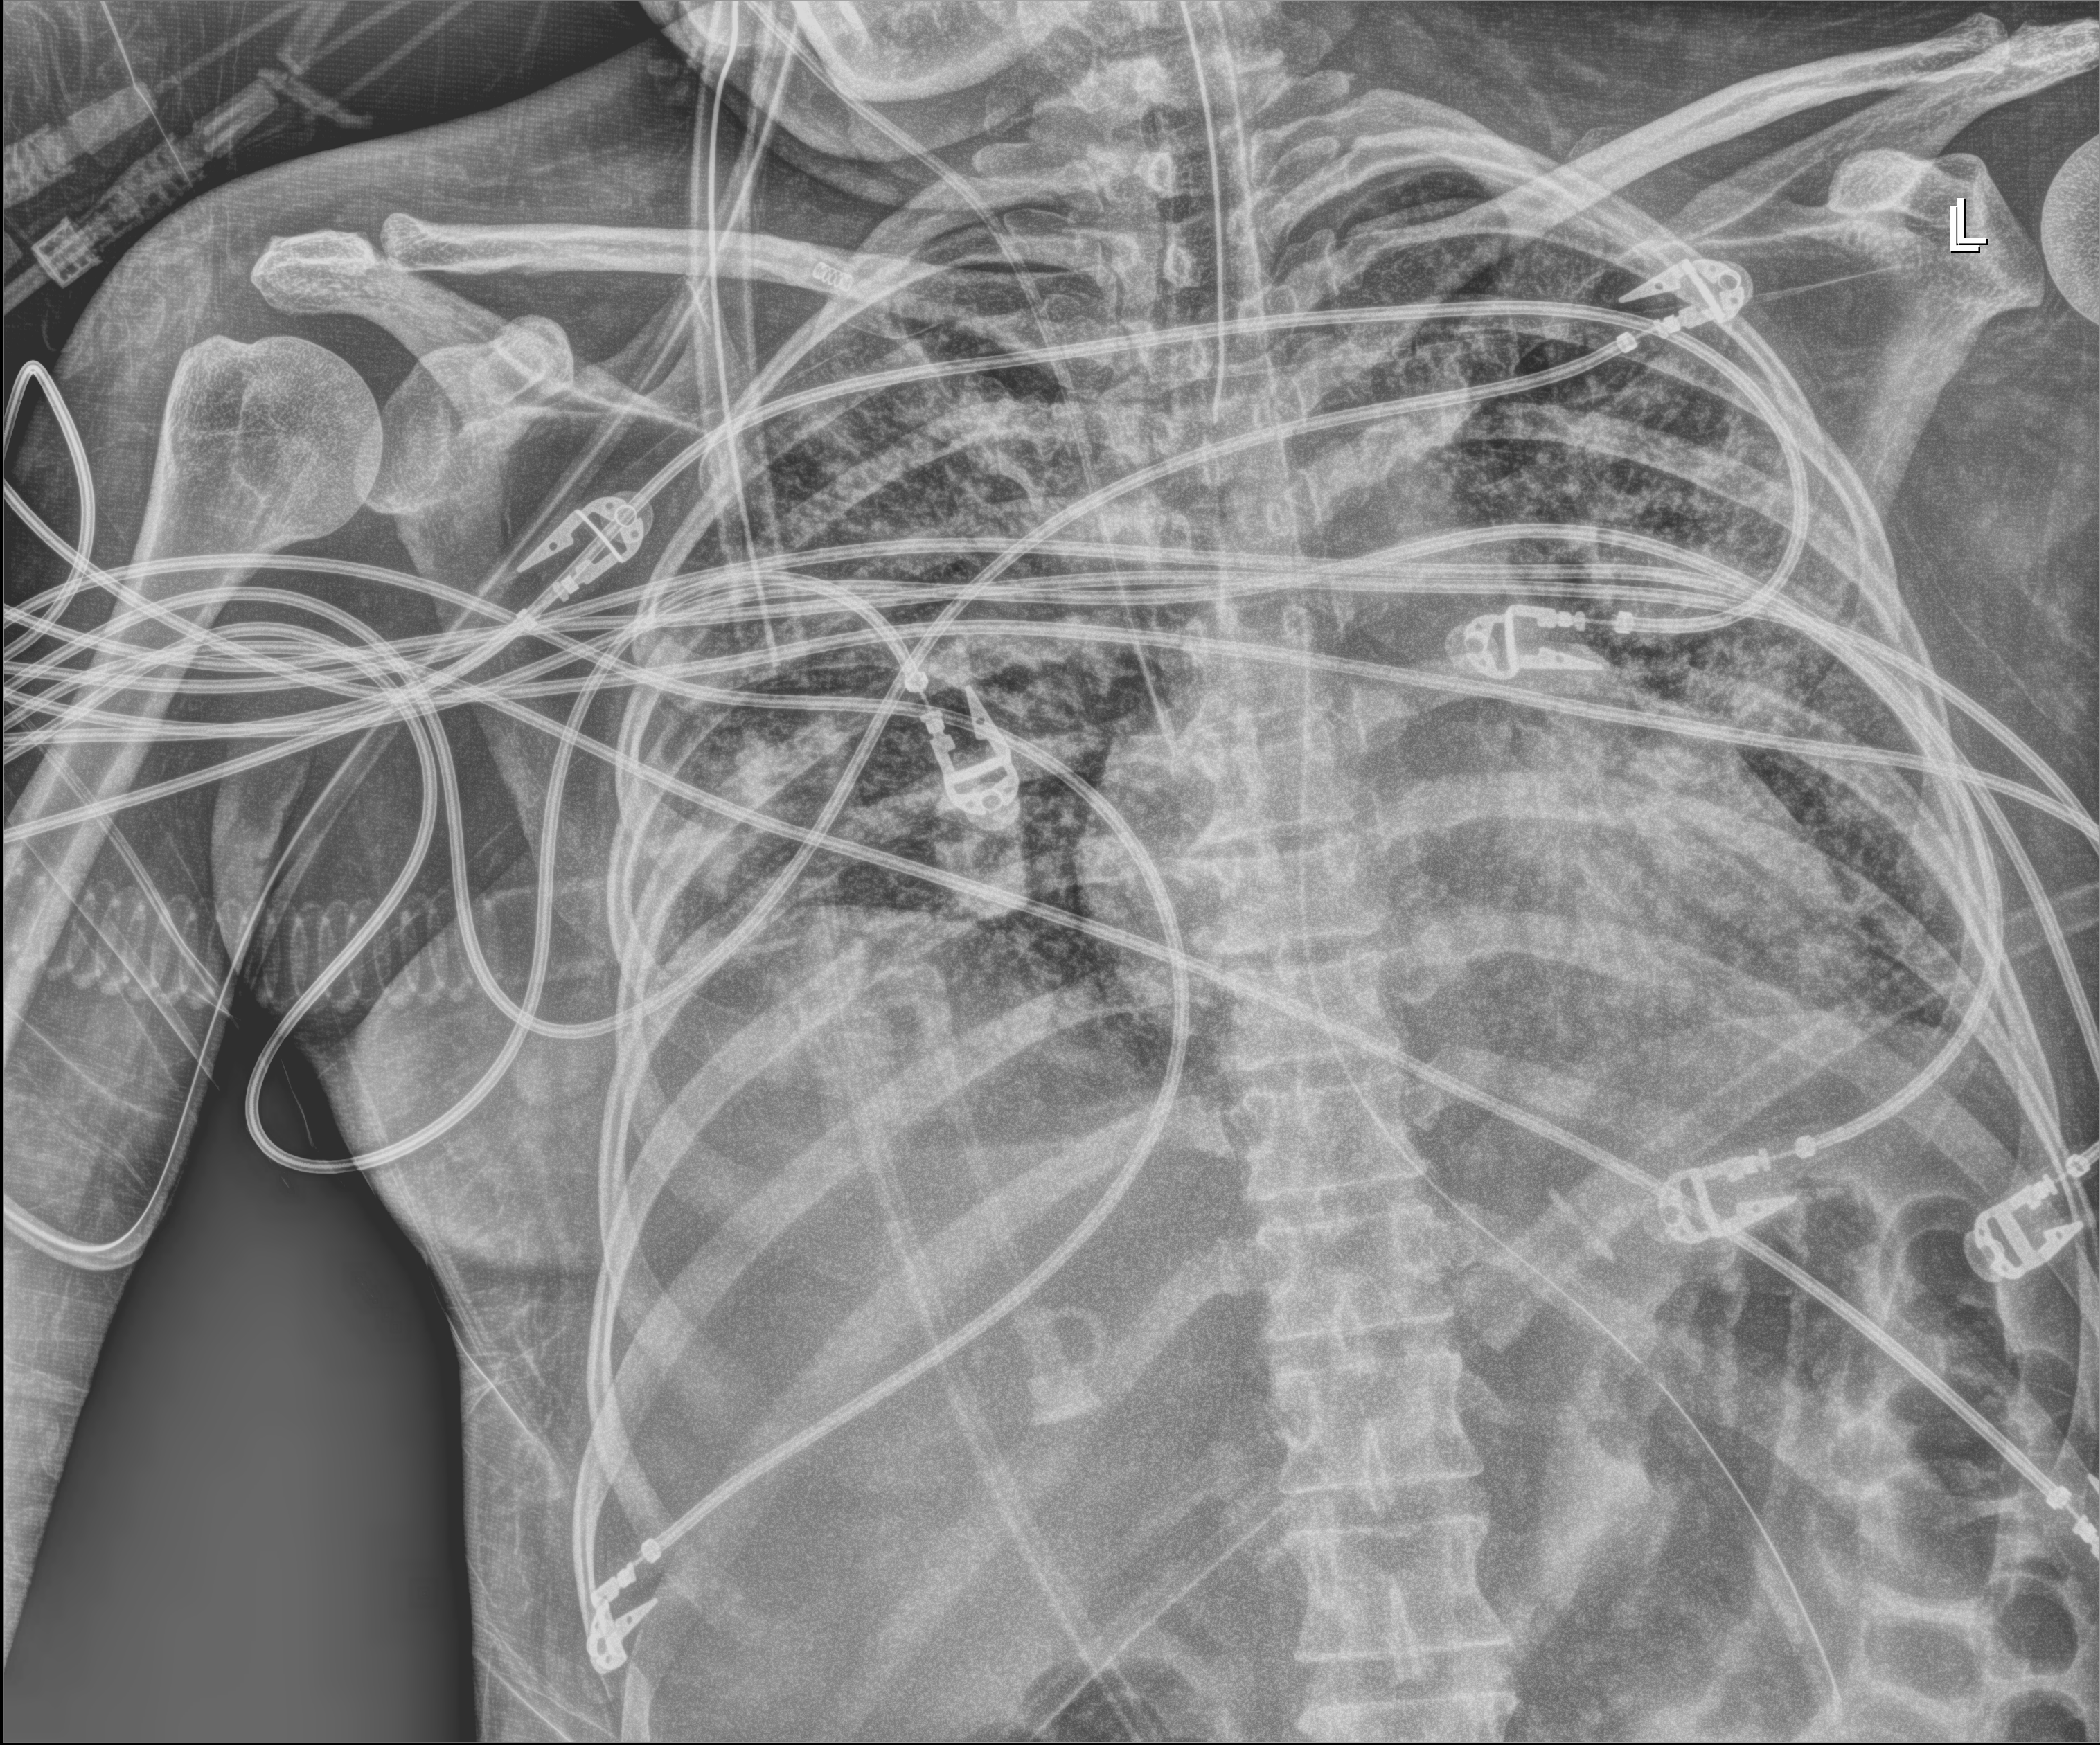
Portable chest radiograph, anteroposterior (AP) projection. Patient hospitalised with COVID-19; female, aged 18–59 years.
From the hospital-stay record, not from the radiograph (when in the stay this image was taken is not recorded): mechanically ventilated during this hospital stay: yes.